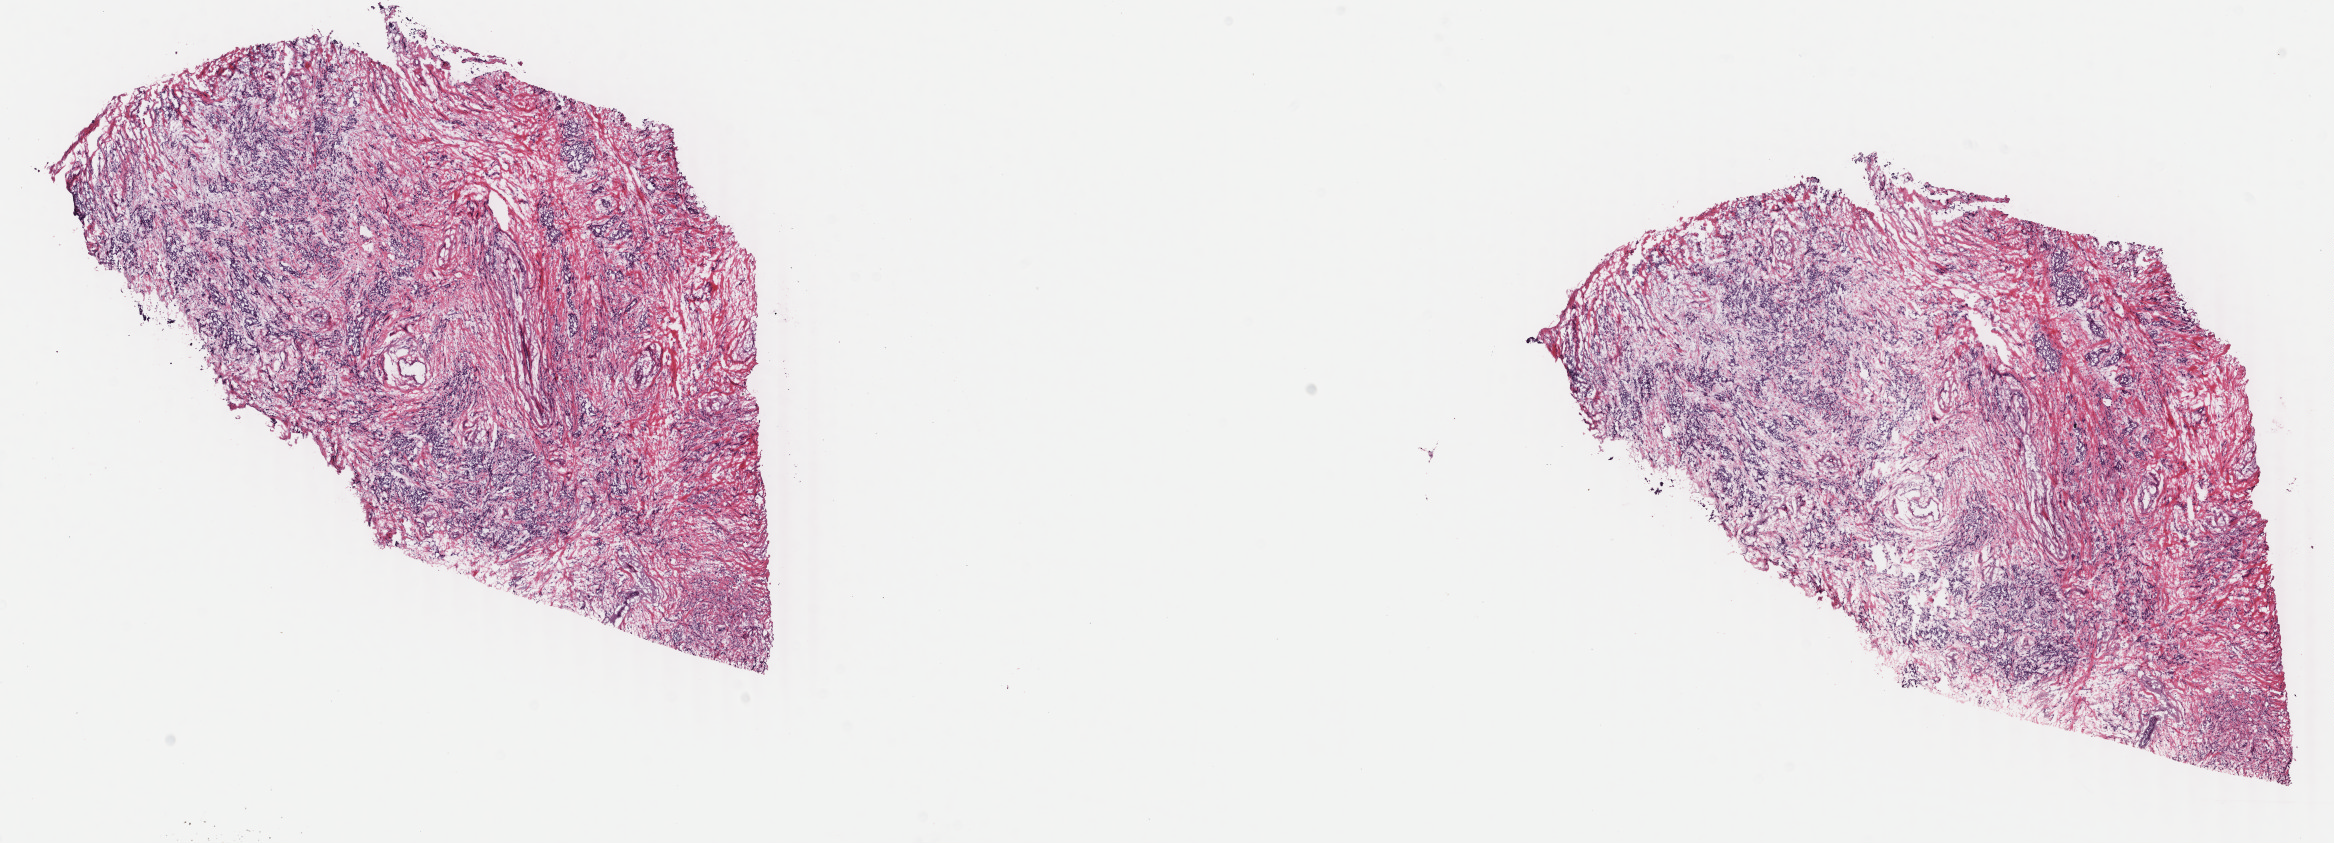
Whole-slide histology image, Hematoxylin and eosin (H&E) stained — whole scanned area (about 18.6 x 6.7 mm) shown as a low-resolution overview. Frozen section from the bottom of the tissue portion. Breast, primary tumour sample. Female, age 54 years at initial diagnosis. Slide review estimates, as recorded: tumour cells 75%, tumour nuclei 75%, normal cells 0%, stromal cells 24%, necrosis 1%. Infiltration values recorded for this section: lymphocyte infiltration 5%, monocyte infiltration 0%, neutrophil infiltration 0%.
Laterality: left. Histologic diagnosis: Infiltrating duct carcinoma, NOS. AJCC pathologic stage: IIIA (7th edition).